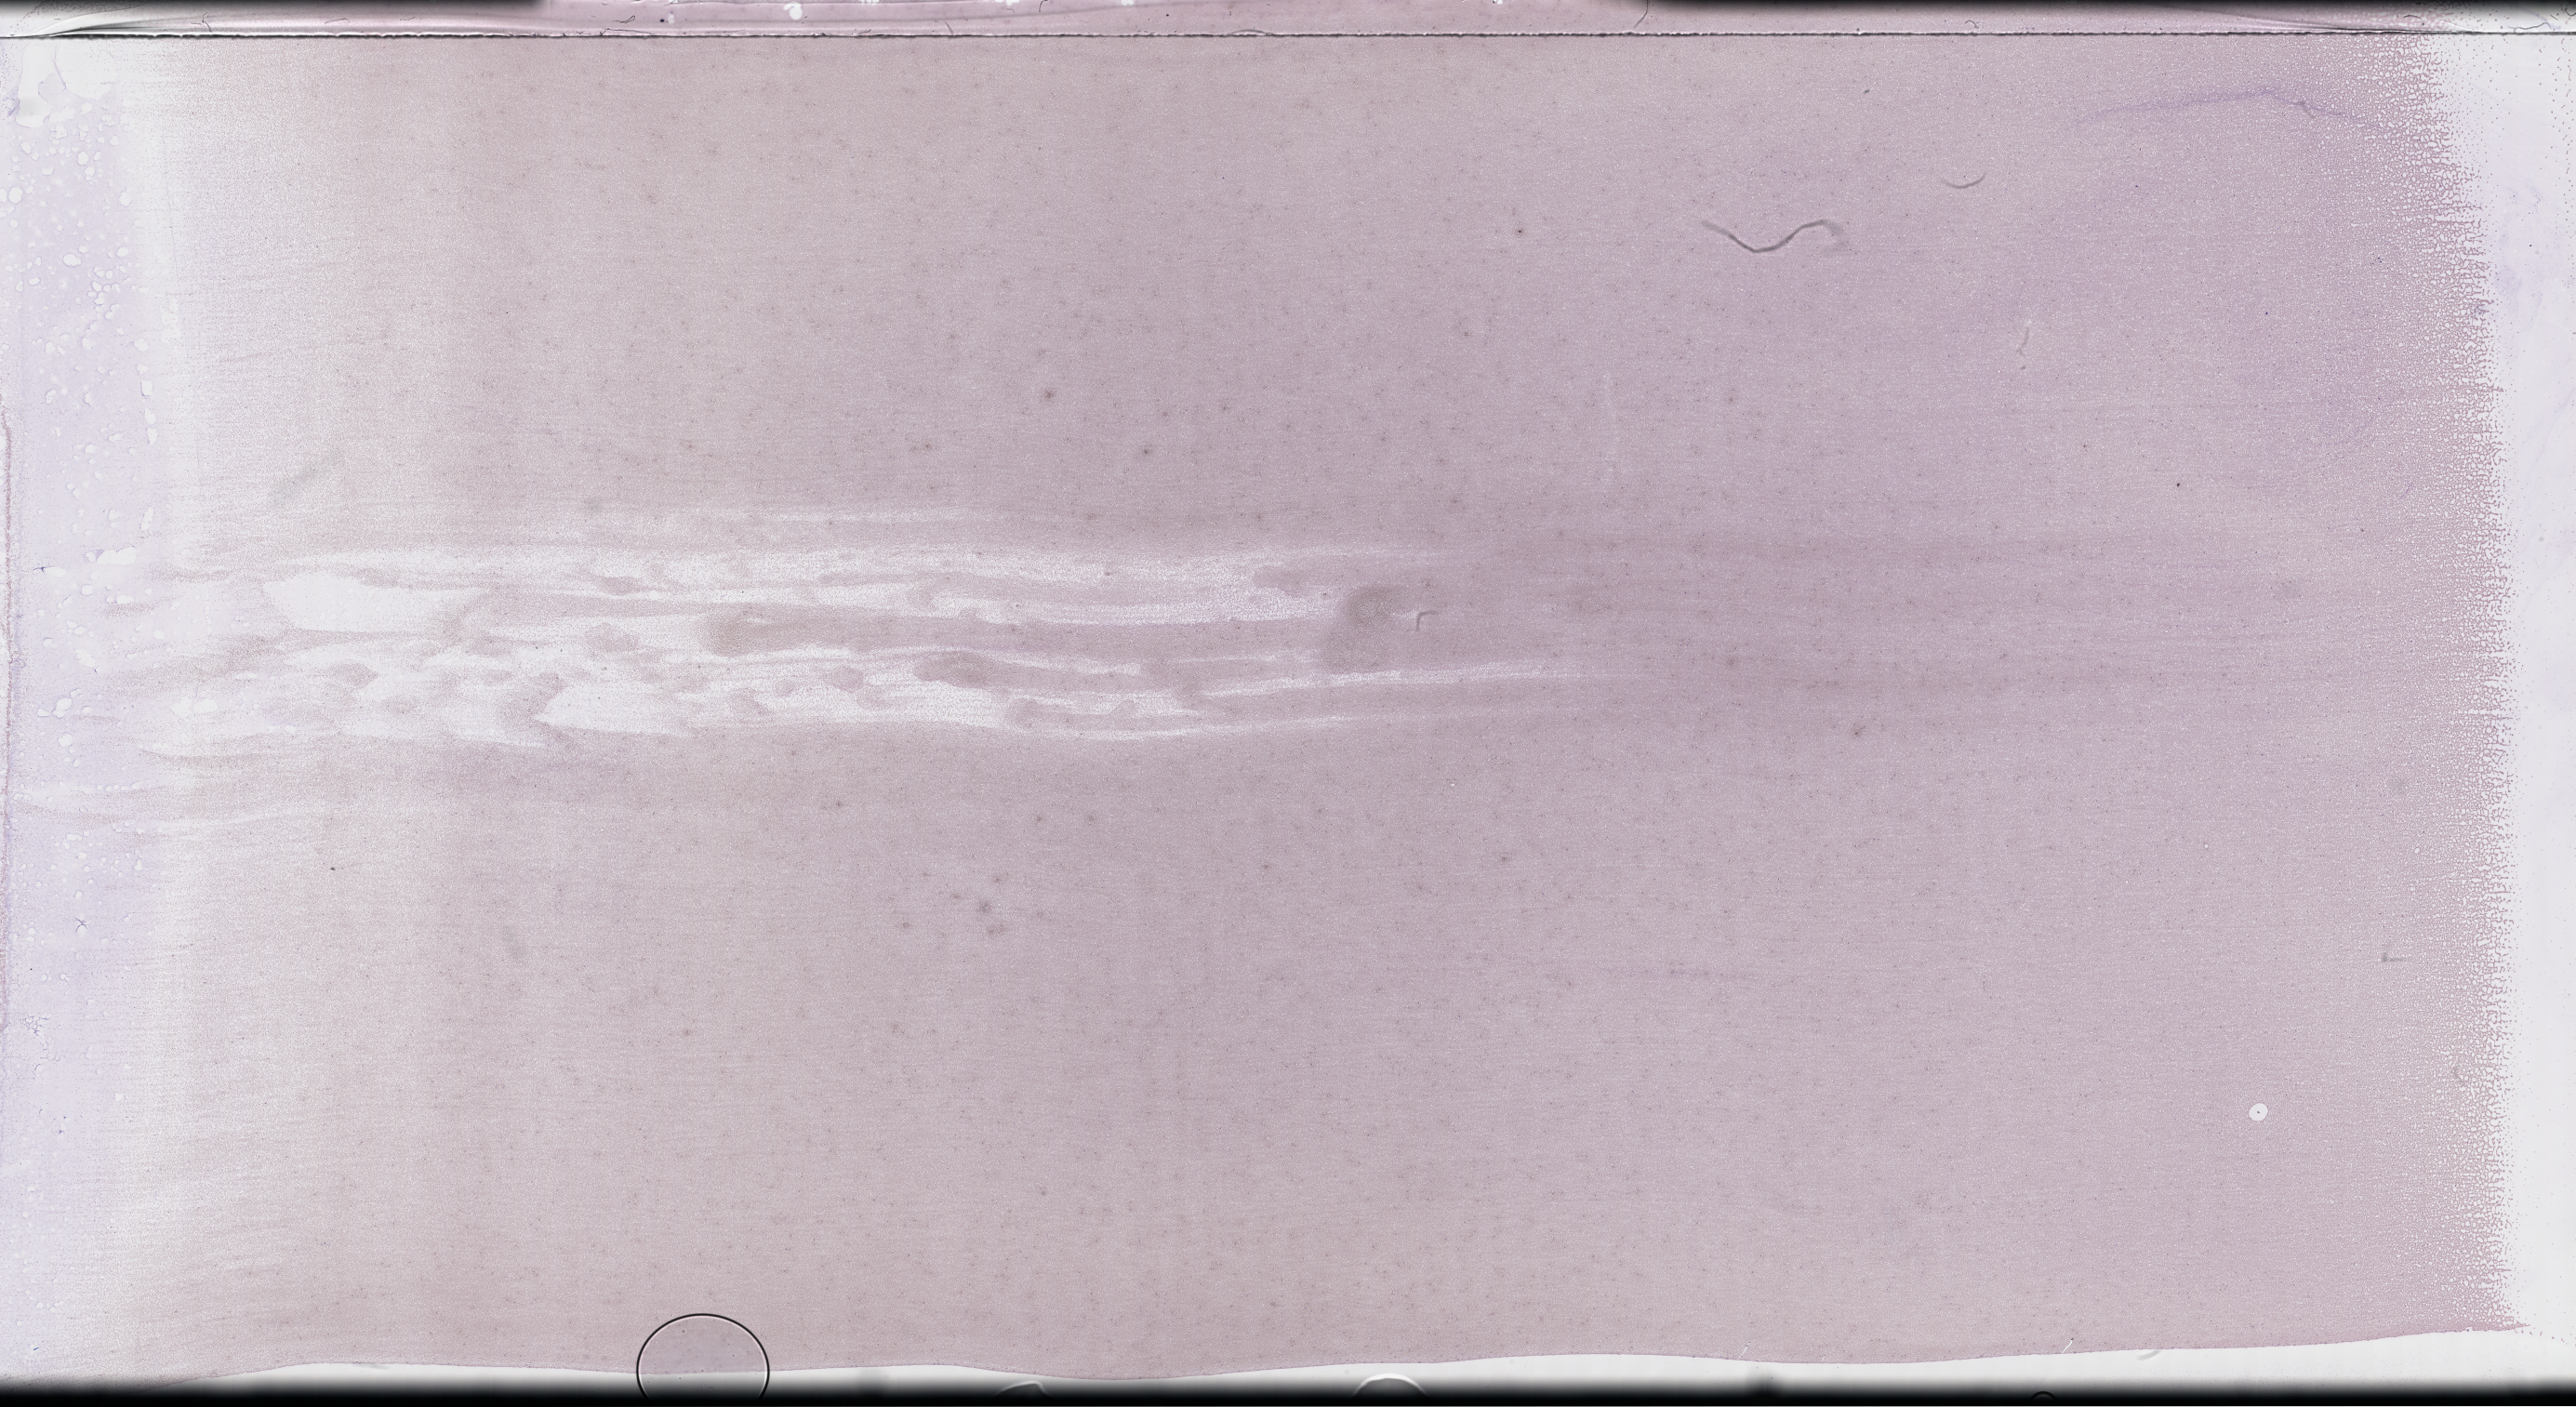
Whole-slide image of a whole blood smear, Wright–Giemsa stain, whole scanned area (about 44.7 x 24.4 mm) shown as a low-resolution overview. Patient sex: female.
From a patient with: Plasma Cell Myeloma.